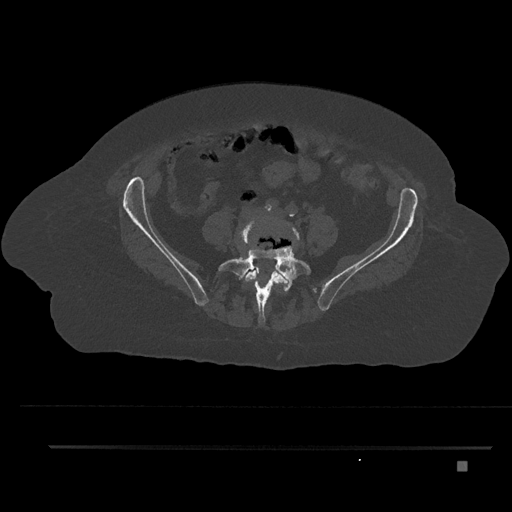
CT including the spine, one axial slice. Slice 51 of 797 in the series (ordered by position). Reconstruction kernel Br40s/3. Bone window (W 1800 / L 400 HU). 0.5 mm slice thickness. 512 × 512 image matrix, field of view 437 × 437 mm. Female patient, age 76 years. Case-level facts recorded for this patient, not image findings: primary cancer: lung; vertebrae with lytic lesions (as recorded): T11, L3.
Annotated regions visible in this slice (semi-automatically segmented with operator editing):
- L4 vertebra: box from (x=238, y=218) to (x=300, y=307) px
- L5 vertebra: (x=218, y=229)–(x=311, y=324)